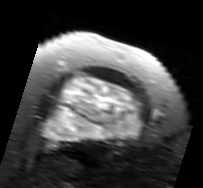
MRI of an extremity soft-tissue mass, one axial slice. T2-weighted fat-saturated. MR volume resampled by the dataset authors to the PET/CT grid (not the native acquisition matrix). 3.27 mm slice thickness. 203 × 188 image matrix, field of view 198 × 184 mm. Female patient. Case-level facts recorded for this patient, not image findings: histological type: malignant solitary fibrous tumor; grade: intermediate; site of the primary tumour: right thigh.
Outlined on this slice (expert contour drawn on MRI and transferred to this co-registered scan by the dataset authors):
- gross tumour volume including surrounding oedema: bounding box (x1, y1, x2, y2) in pixels: (42, 72, 146, 146)
- gross tumour volume (mass): (42, 76, 143, 146)